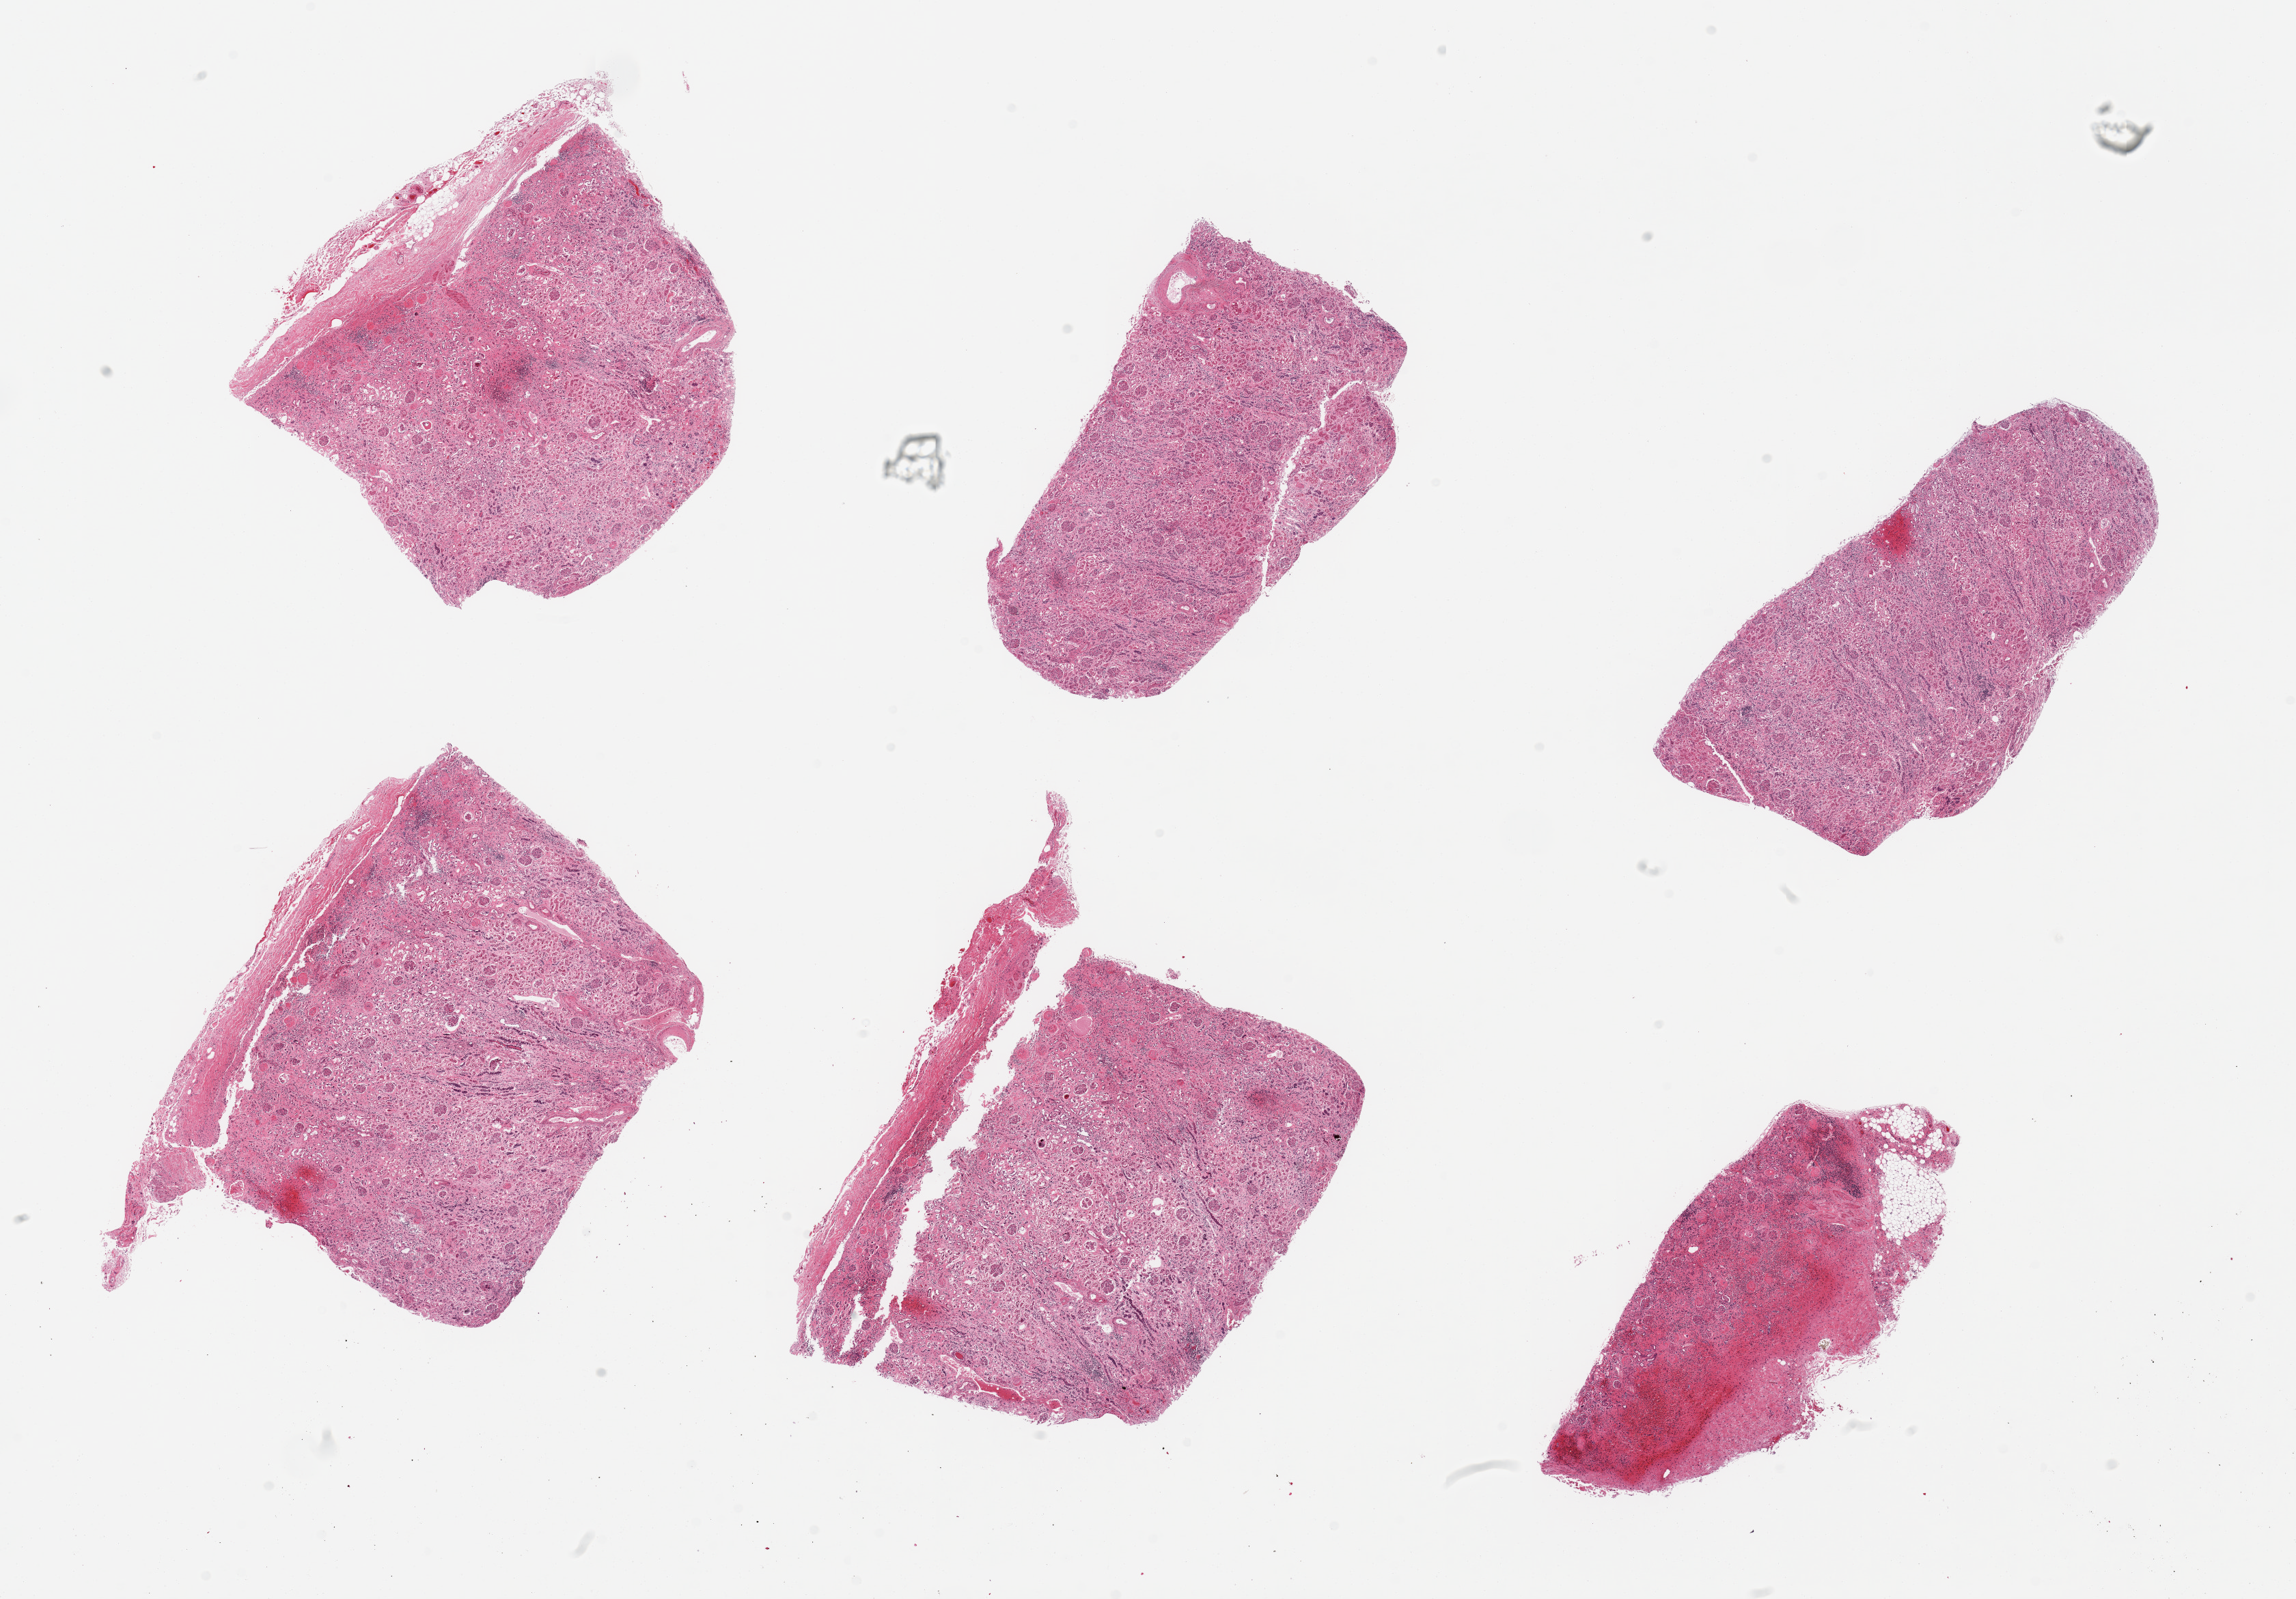
Whole-slide image, hematoxylin and eosin (H&E) stain — whole scanned area (about 26.6 x 18.5 mm, acquisition: 20x scan) shown as a low-resolution overview, PAXgene-fixed paraffin-embedded (PFPE) section, section of renal cortex (target tissue), donor tissue sample. Female donor.
• pathologist's review note for this sample: 6 pieces; moderate degree of chronic pyelonephritis